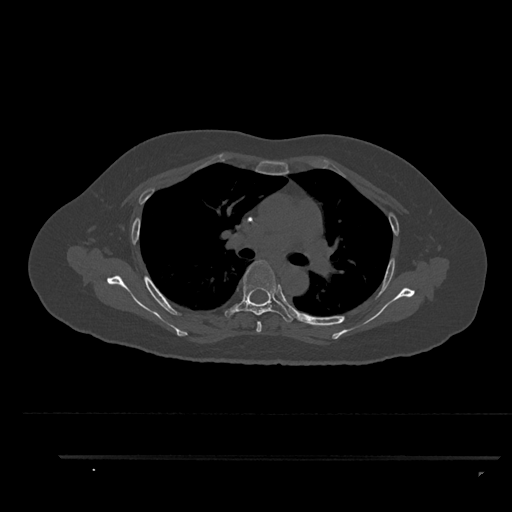
CT including the spine, one axial slice; slice 609 of 797 in the series (ordered by position); bone window (W 1800 / L 400 HU); 512 × 512 image matrix. Patient: female, 44 years. From the clinical record (not read from this slice): primary cancer: renal.
Annotated regions visible in this slice (semi-automatic segmentation, software-assisted and operator-edited):
- T4 vertebra: box from (x=256, y=321) to (x=262, y=333) px
- T5 vertebra: (x=224, y=260)–(x=294, y=322)